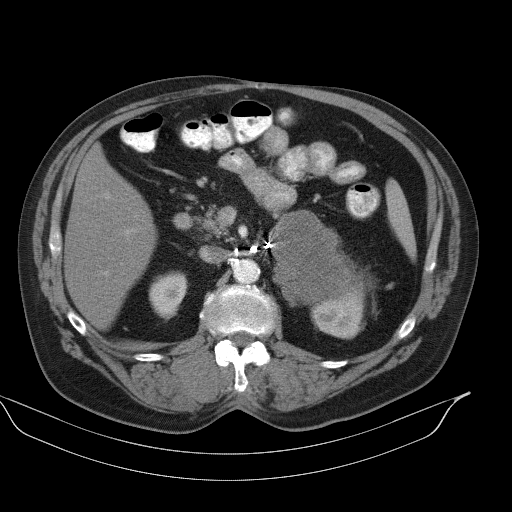
Contrast-enhanced abdominal CT, one axial slice; position 61 of 92 along the scan axis; intravenous contrast given; soft-tissue window (W 400 / L 40 HU); 5 mm slice thickness; 512 × 512 image matrix, field of view 449 × 449 mm. Patient: male, 56 years. From the clinical record (not read from this slice): diagnosis: adrenocortical carcinoma; tumour side: left adrenal; tumour size at pathology: 15 cm; Ki-67 index: 35 %; stage (as recorded): 4.
Outlined on this slice (semi-automatically segmented with operator editing):
- mass: bounding box (x1, y1, x2, y2) in pixels: (273, 212, 361, 302)